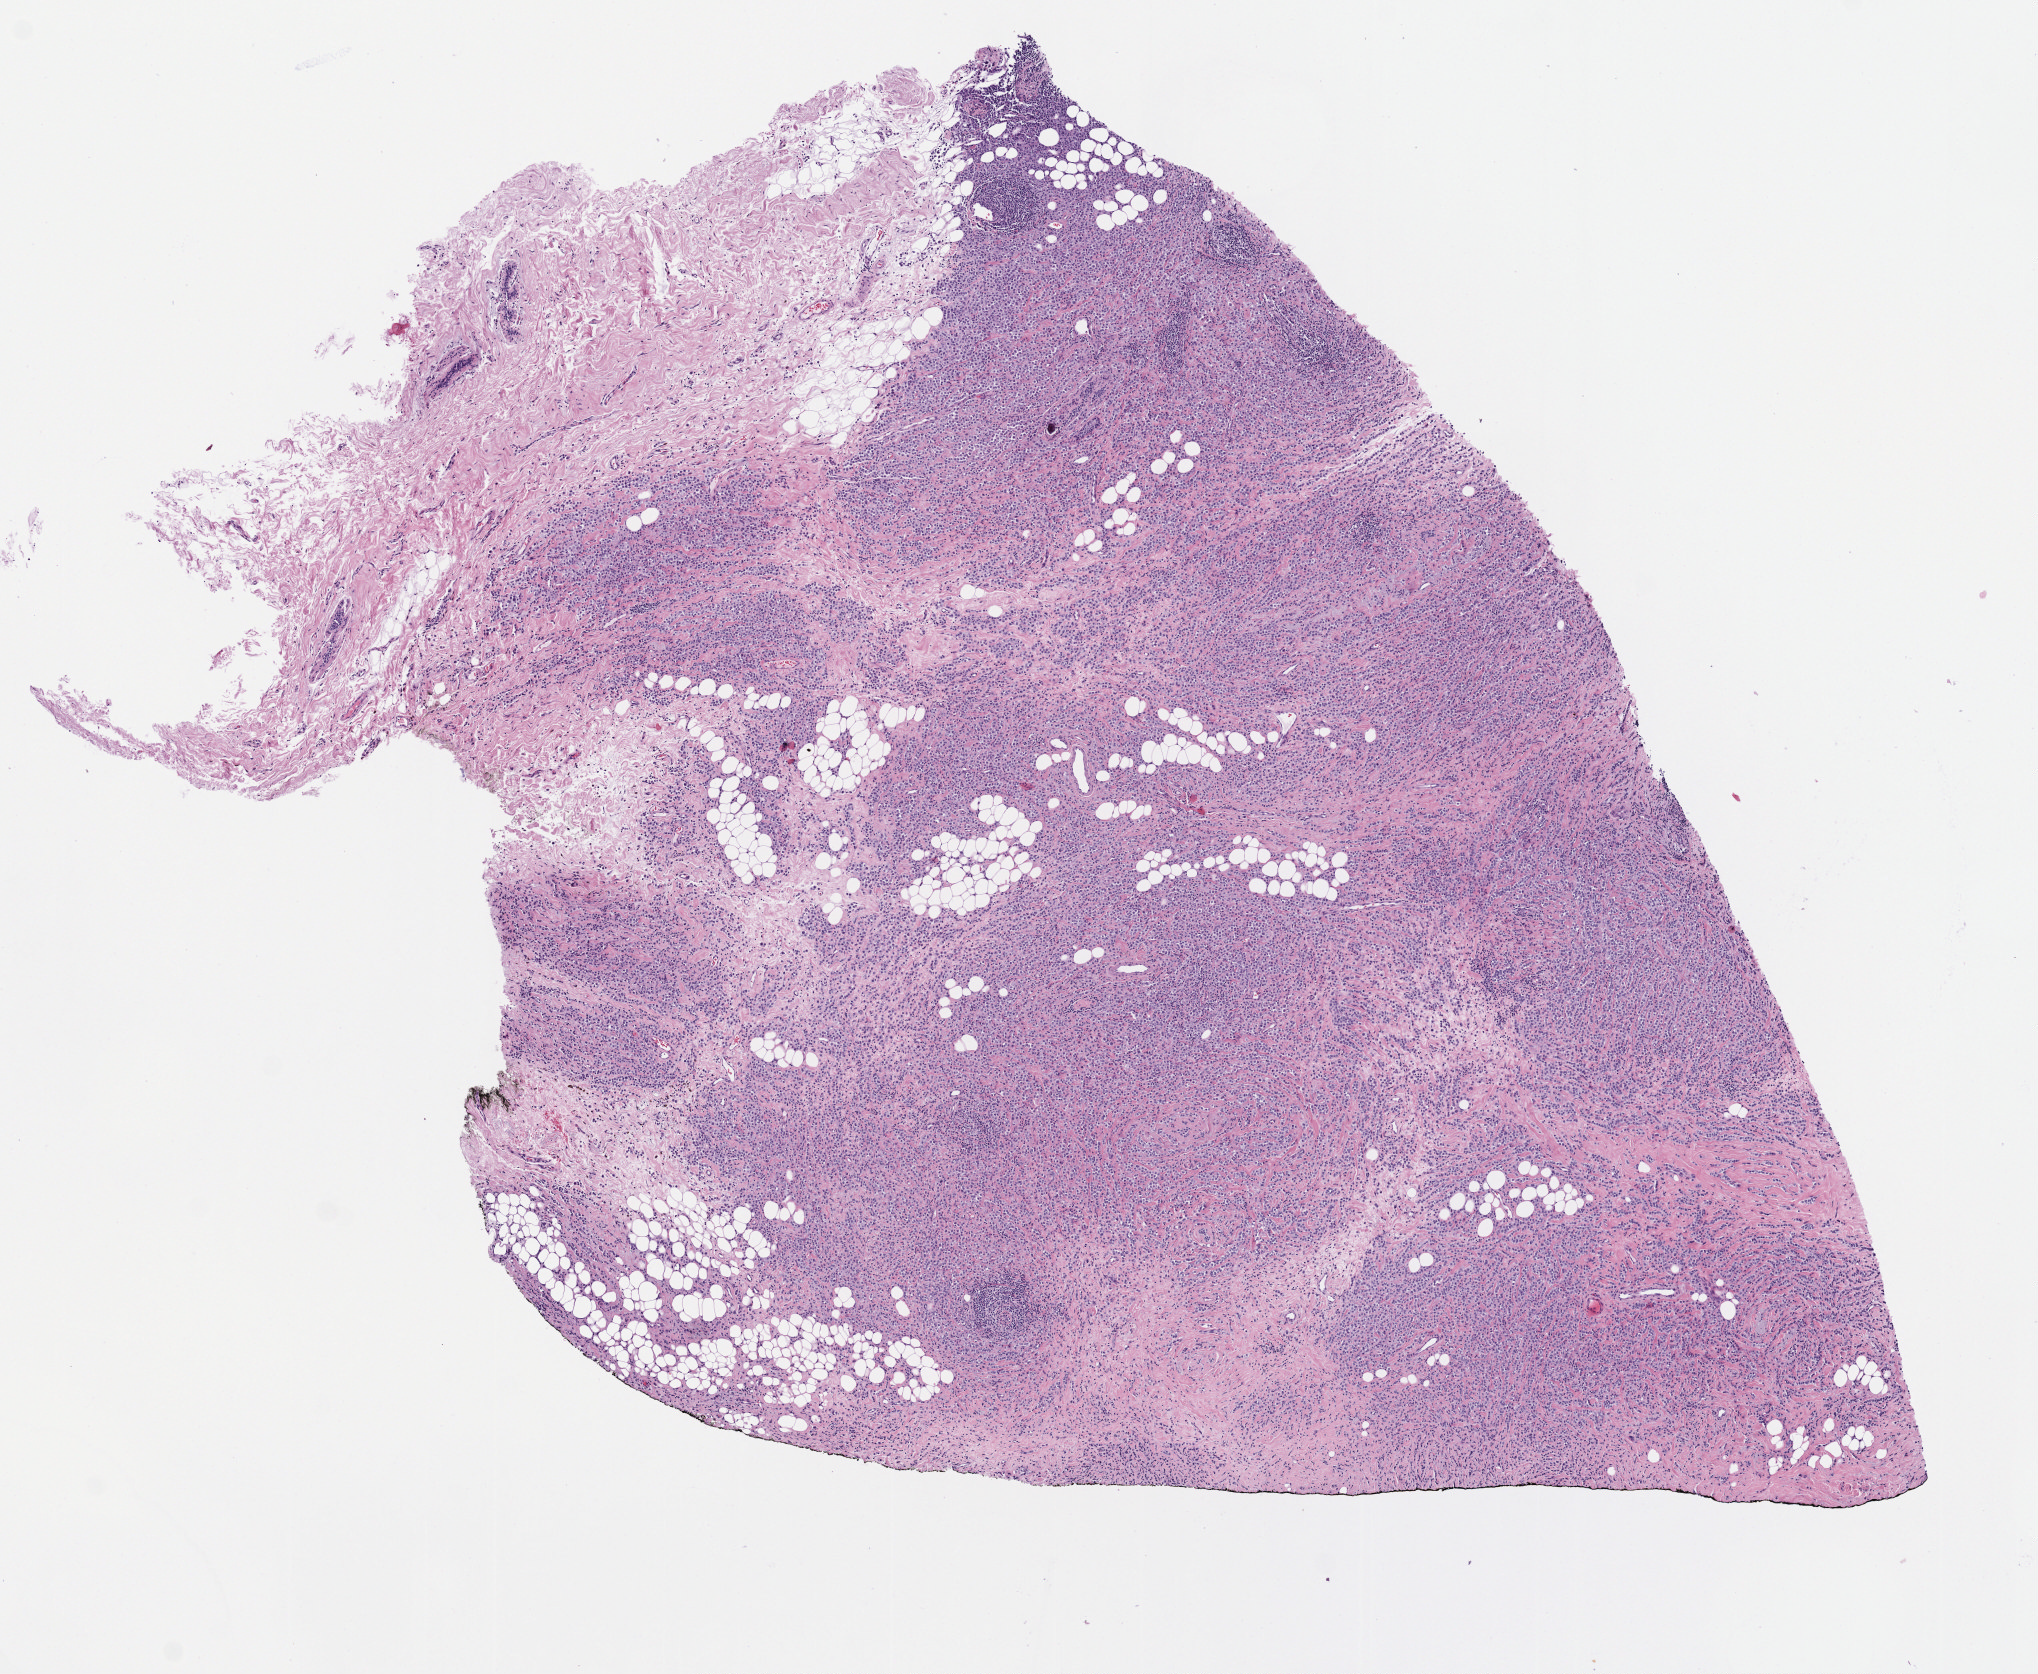
H&E-stained whole-slide image — a low-resolution overview of the entire scanned area, about 8.2 x 6.8 mm (acquisition: 40x scan), formalin-fixed paraffin-embedded (FFPE) diagnostic section, primary tumour sample from the breast. Female patient; age at initial diagnosis 74 years.
Lymph nodes positive (case pathology): 0 of 8 examined. Pathologic diagnosis: Lobular carcinoma, NOS. TNM: T2 N0 MX. AJCC pathologic stage: IIA (7th edition).